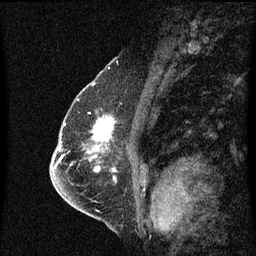
Breast MRI (dynamic contrast-enhanced), one sagittal slice; slice 40 of 60 in the series (ordered by position); dynamic contrast-enhanced series, image 2 of 3 at this slice position (ordered by acquisition); 1.5 T; TE 4.2 ms, TR 8.4 ms; 2 mm slice thickness; 256 × 256 image matrix, field of view 200 × 200 mm. Patient: female, 57 years. From the clinical record (not read from this slice): setting: breast cancer imaged before/during neoadjuvant chemotherapy; receptor status: HR-positive, HER2-negative.
Structures marked on this image (semi-automatic segmentation, software-assisted and operator-edited):
- analysis volume of interest (the breast-tissue region the enhancement analysis was run in; not a lesion): bounding box <94,110,116,145> (left, top, right, bottom; pixels)
- tumour enhancement mask (voxels above the 70 % enhancement threshold inside the analysis volume of interest): <94,118,115,141>